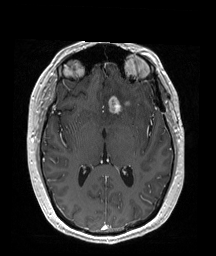
Brain MRI from a brain-tumour surgery series, one axial slice. Position 98 of 192 along the scan axis. T1-weighted post-contrast. 216 × 256 image matrix, field of view 211 × 250 mm. Case-level facts recorded for this patient, not image findings: histopathology: Oligodendroglioma; WHO grade: 2; IDH mutation: yes; tumour location: Left Frontal (septal).
Outlined on this slice (expert manual segmentation):
- tumour: bounding box <107,95,132,117> (left, top, right, bottom; pixels)